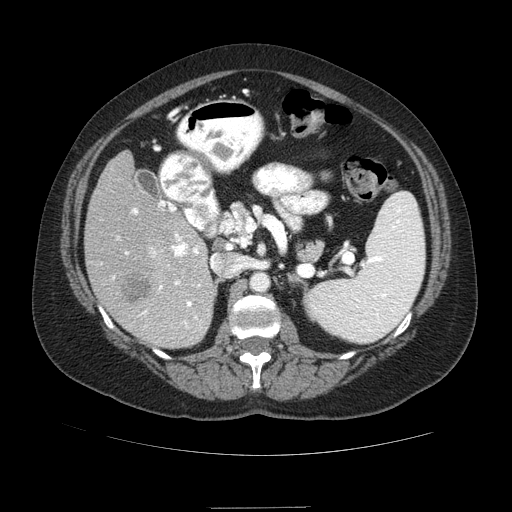
Contrast-enhanced abdominal CT (liver protocol), one axial slice. Slice 42 of 89 in the series (ordered by position). Reconstruction kernel STANDARD. 120 kVp. Soft-tissue window (W 400 / L 40 HU). 512 × 512 image matrix. From the clinical record (not read from this slice): diagnosis: hepatocellular carcinoma (patient treated with transarterial chemoembolisation; whether this scan precedes or follows treatment is not stated here); TNM stage (as recorded): Stage-IIIB; Child-Pugh class: A.
Outlined on this slice (semi-automatic segmentation, software-assisted and operator-edited):
- liver parenchyma outside the tumour (the mass and vessels are separate outlines, so this box may not span the whole liver): bounding box <84,152,216,348> (left, top, right, bottom; pixels)
- mass: <122,270,151,302>
- liver vessels: <112,200,200,328>